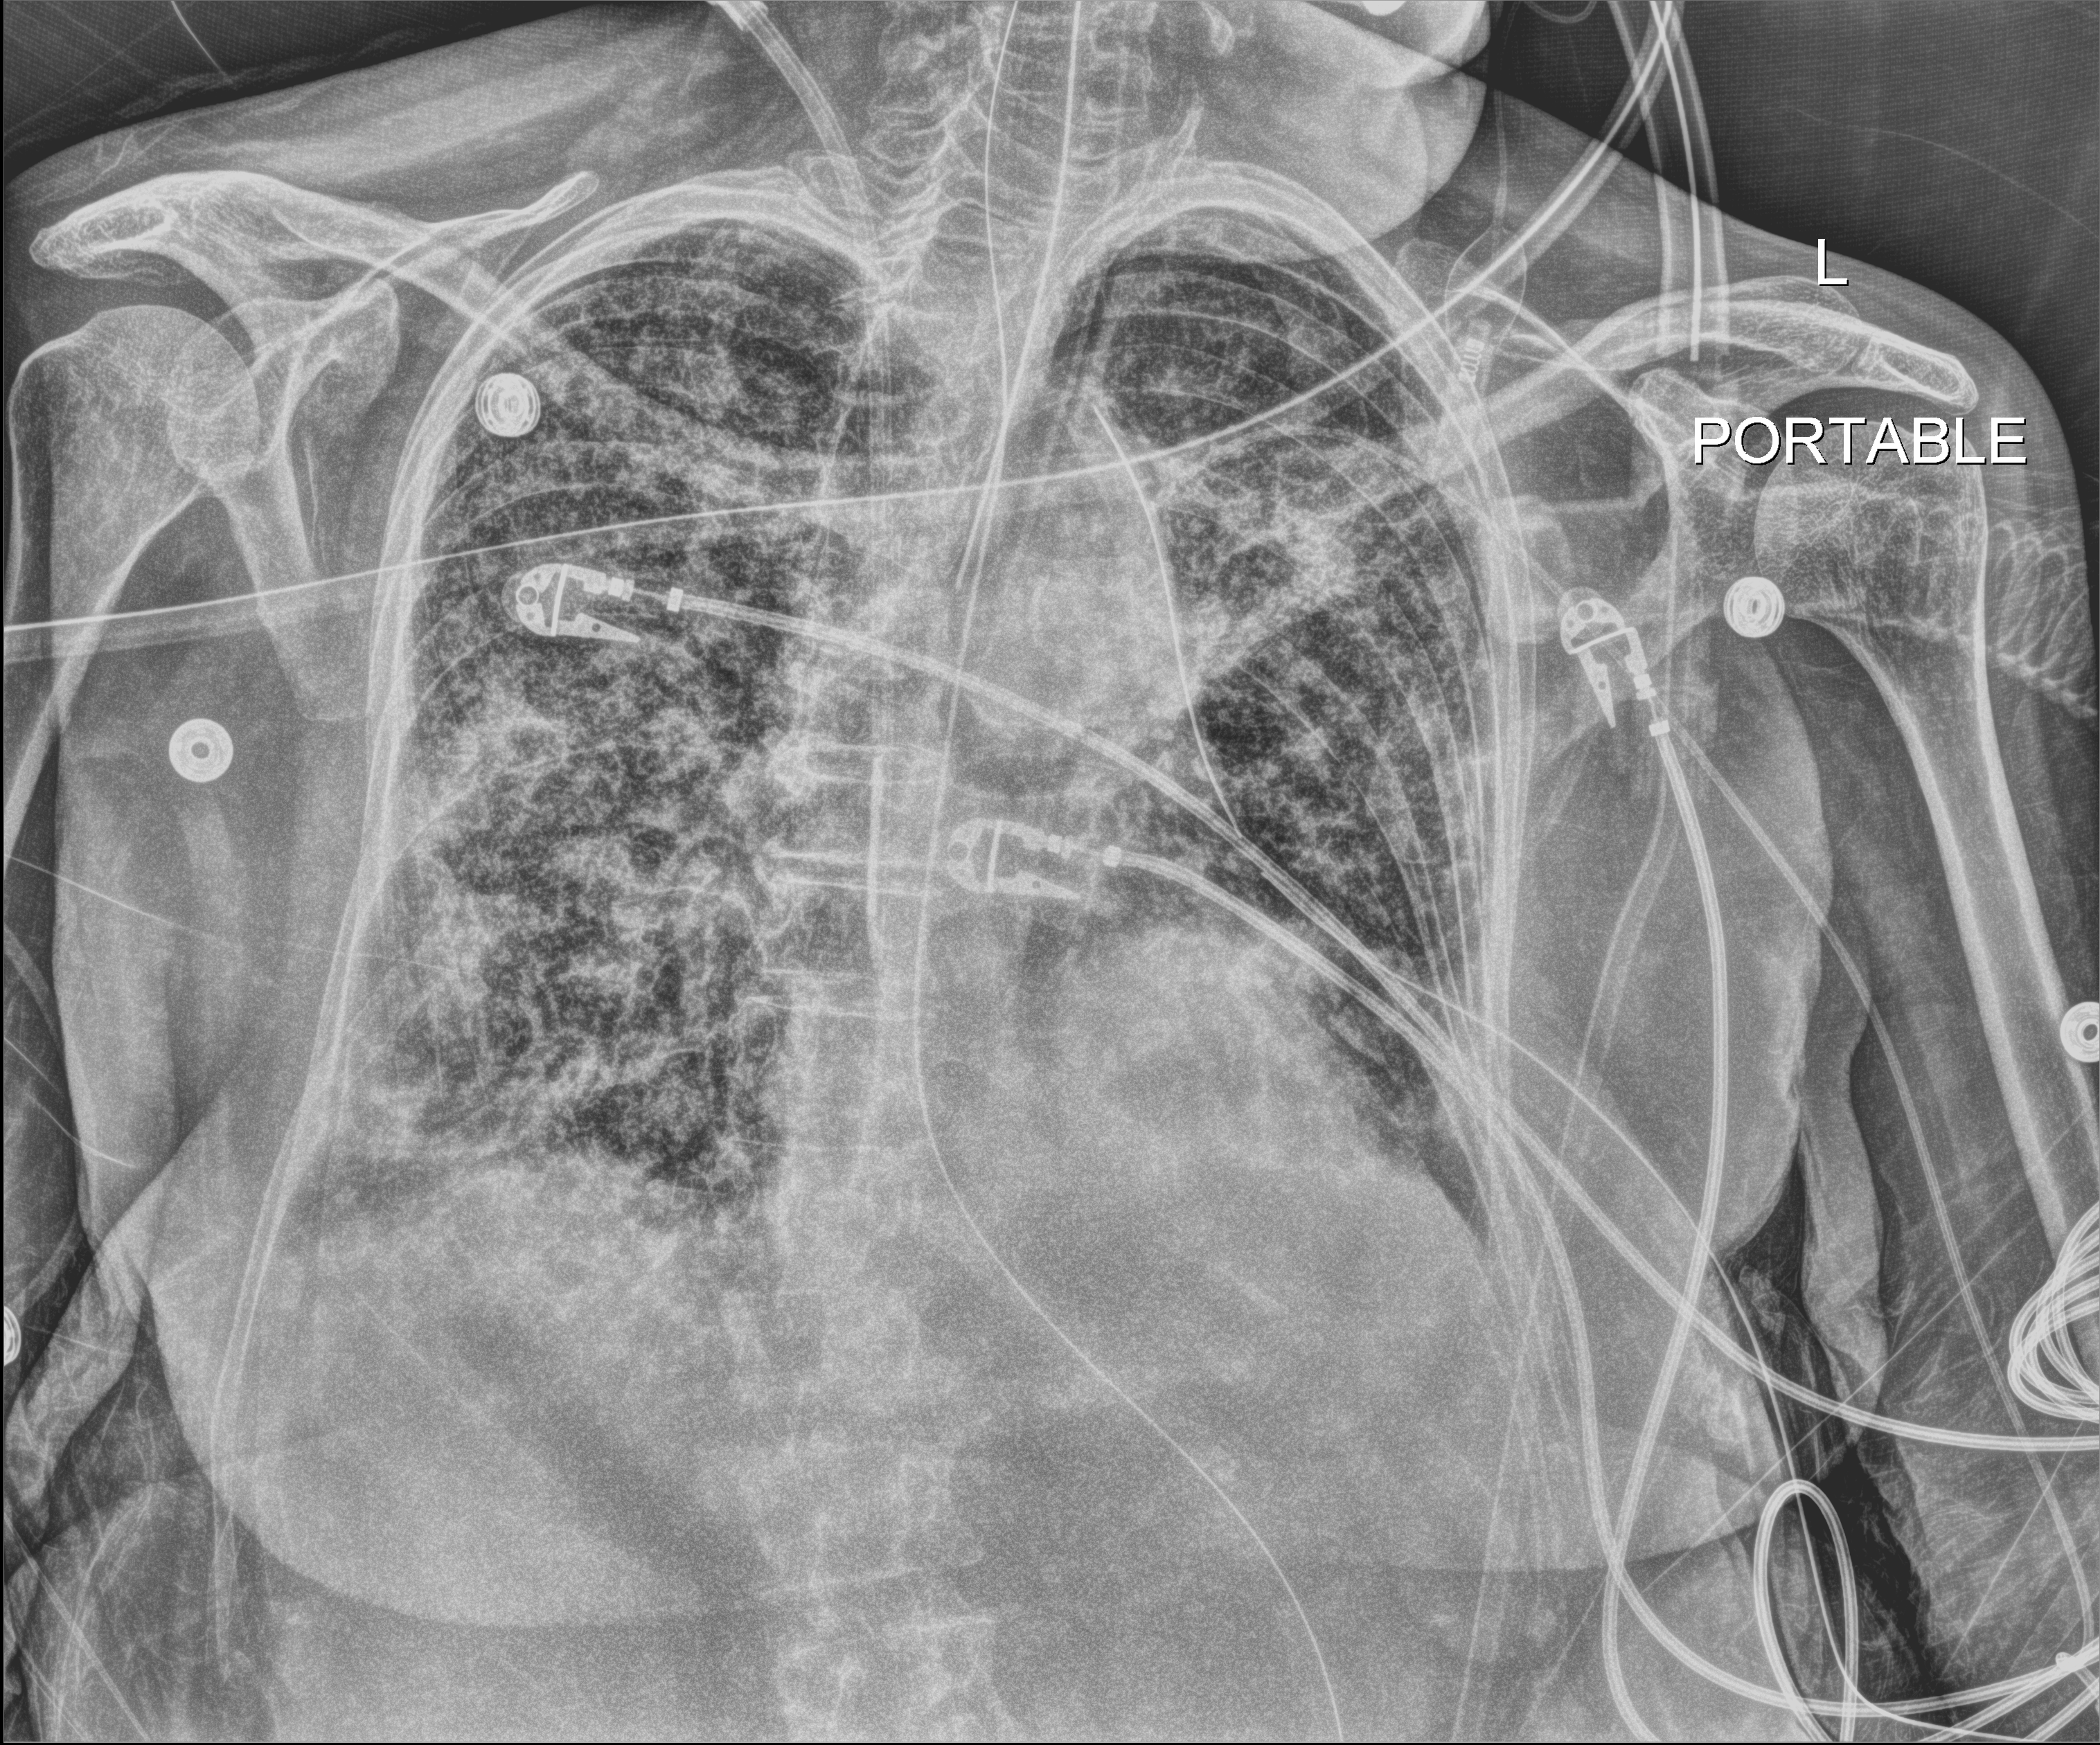
Chest X-ray (portable); anteroposterior (AP) projection. Patient hospitalised with COVID-19; female, aged 75–90 years.
Admission-level facts for this patient (not findings on this image; timing relative to this image not recorded): COPD (admission record): no; admitted to intensive care during this hospital stay: yes.